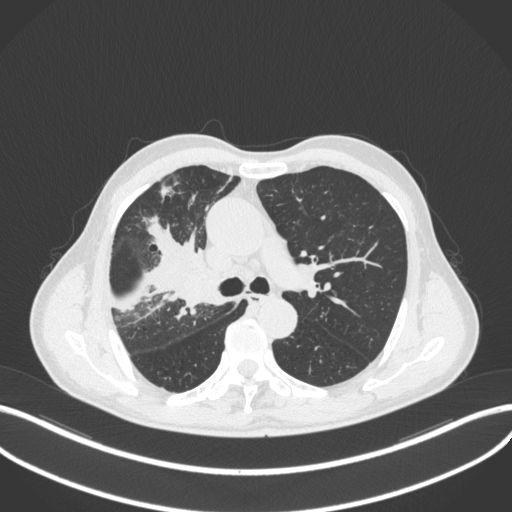
Chest CT, one axial slice. Slice 318 of 490 in the series (ordered by position). 120 kVp. Lung window (W 1500 / L -600 HU). 512 × 512 image matrix. Male patient, age 69 years. From the clinical record (not read from this slice): clinical TNM (as recorded): T2a N0 M0.
Annotated regions visible in this slice (rectangle marked by the reading radiologist):
- lung tumour (recorded histology: adenocarcinoma): bounding box <165,264,223,315> (left, top, right, bottom; pixels)